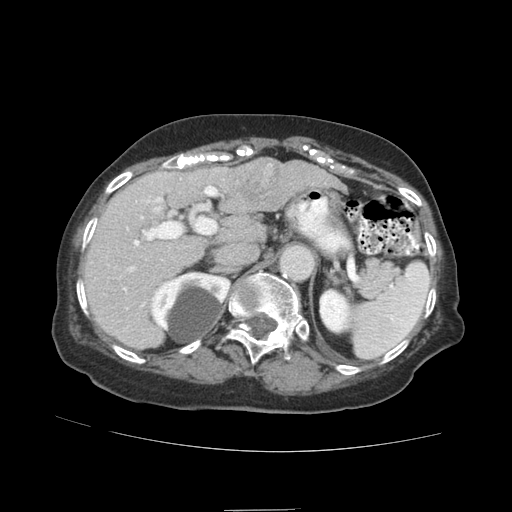
Contrast-enhanced abdominal CT (liver protocol), one axial slice. Position 56 of 89 along the scan axis. Reconstruction kernel STANDARD. Soft-tissue window (W 400 / L 40 HU). 2.5 mm slice thickness. 512 × 512 image matrix, field of view 360 × 360 mm. Case-level facts recorded for this patient, not image findings: diagnosis: hepatocellular carcinoma (patient treated with transarterial chemoembolisation; whether this scan precedes or follows treatment is not stated here); TNM stage (as recorded): Stage-II; Child-Pugh class: A; tumour differentiation: moderately differentiated; tumour nodularity: multinodular.
Outlined on this slice (semi-automatically segmented with operator editing):
- liver parenchyma outside the tumour (the mass and vessels are separate outlines, so this box may not span the whole liver): bounding box [x1, y1, x2, y2] px = [84, 160, 332, 348]
- mass: [229, 157, 291, 212]
- liver vessels: [94, 170, 218, 341]